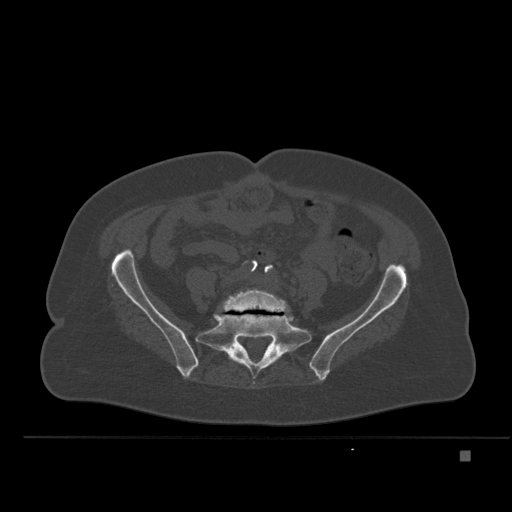
CT including the spine, one axial slice; position 151 of 477 along the scan axis; bone window (W 1800 / L 400 HU); 1.5 mm slice thickness; 512 × 512 image matrix, field of view 422 × 422 mm. Patient: female, 74 years. Case-level facts recorded for this patient, not image findings: primary cancer: colon.
Structures marked on this image (semi-automatically segmented with operator editing):
- L5 vertebra: box from (x=223, y=280) to (x=288, y=312) px